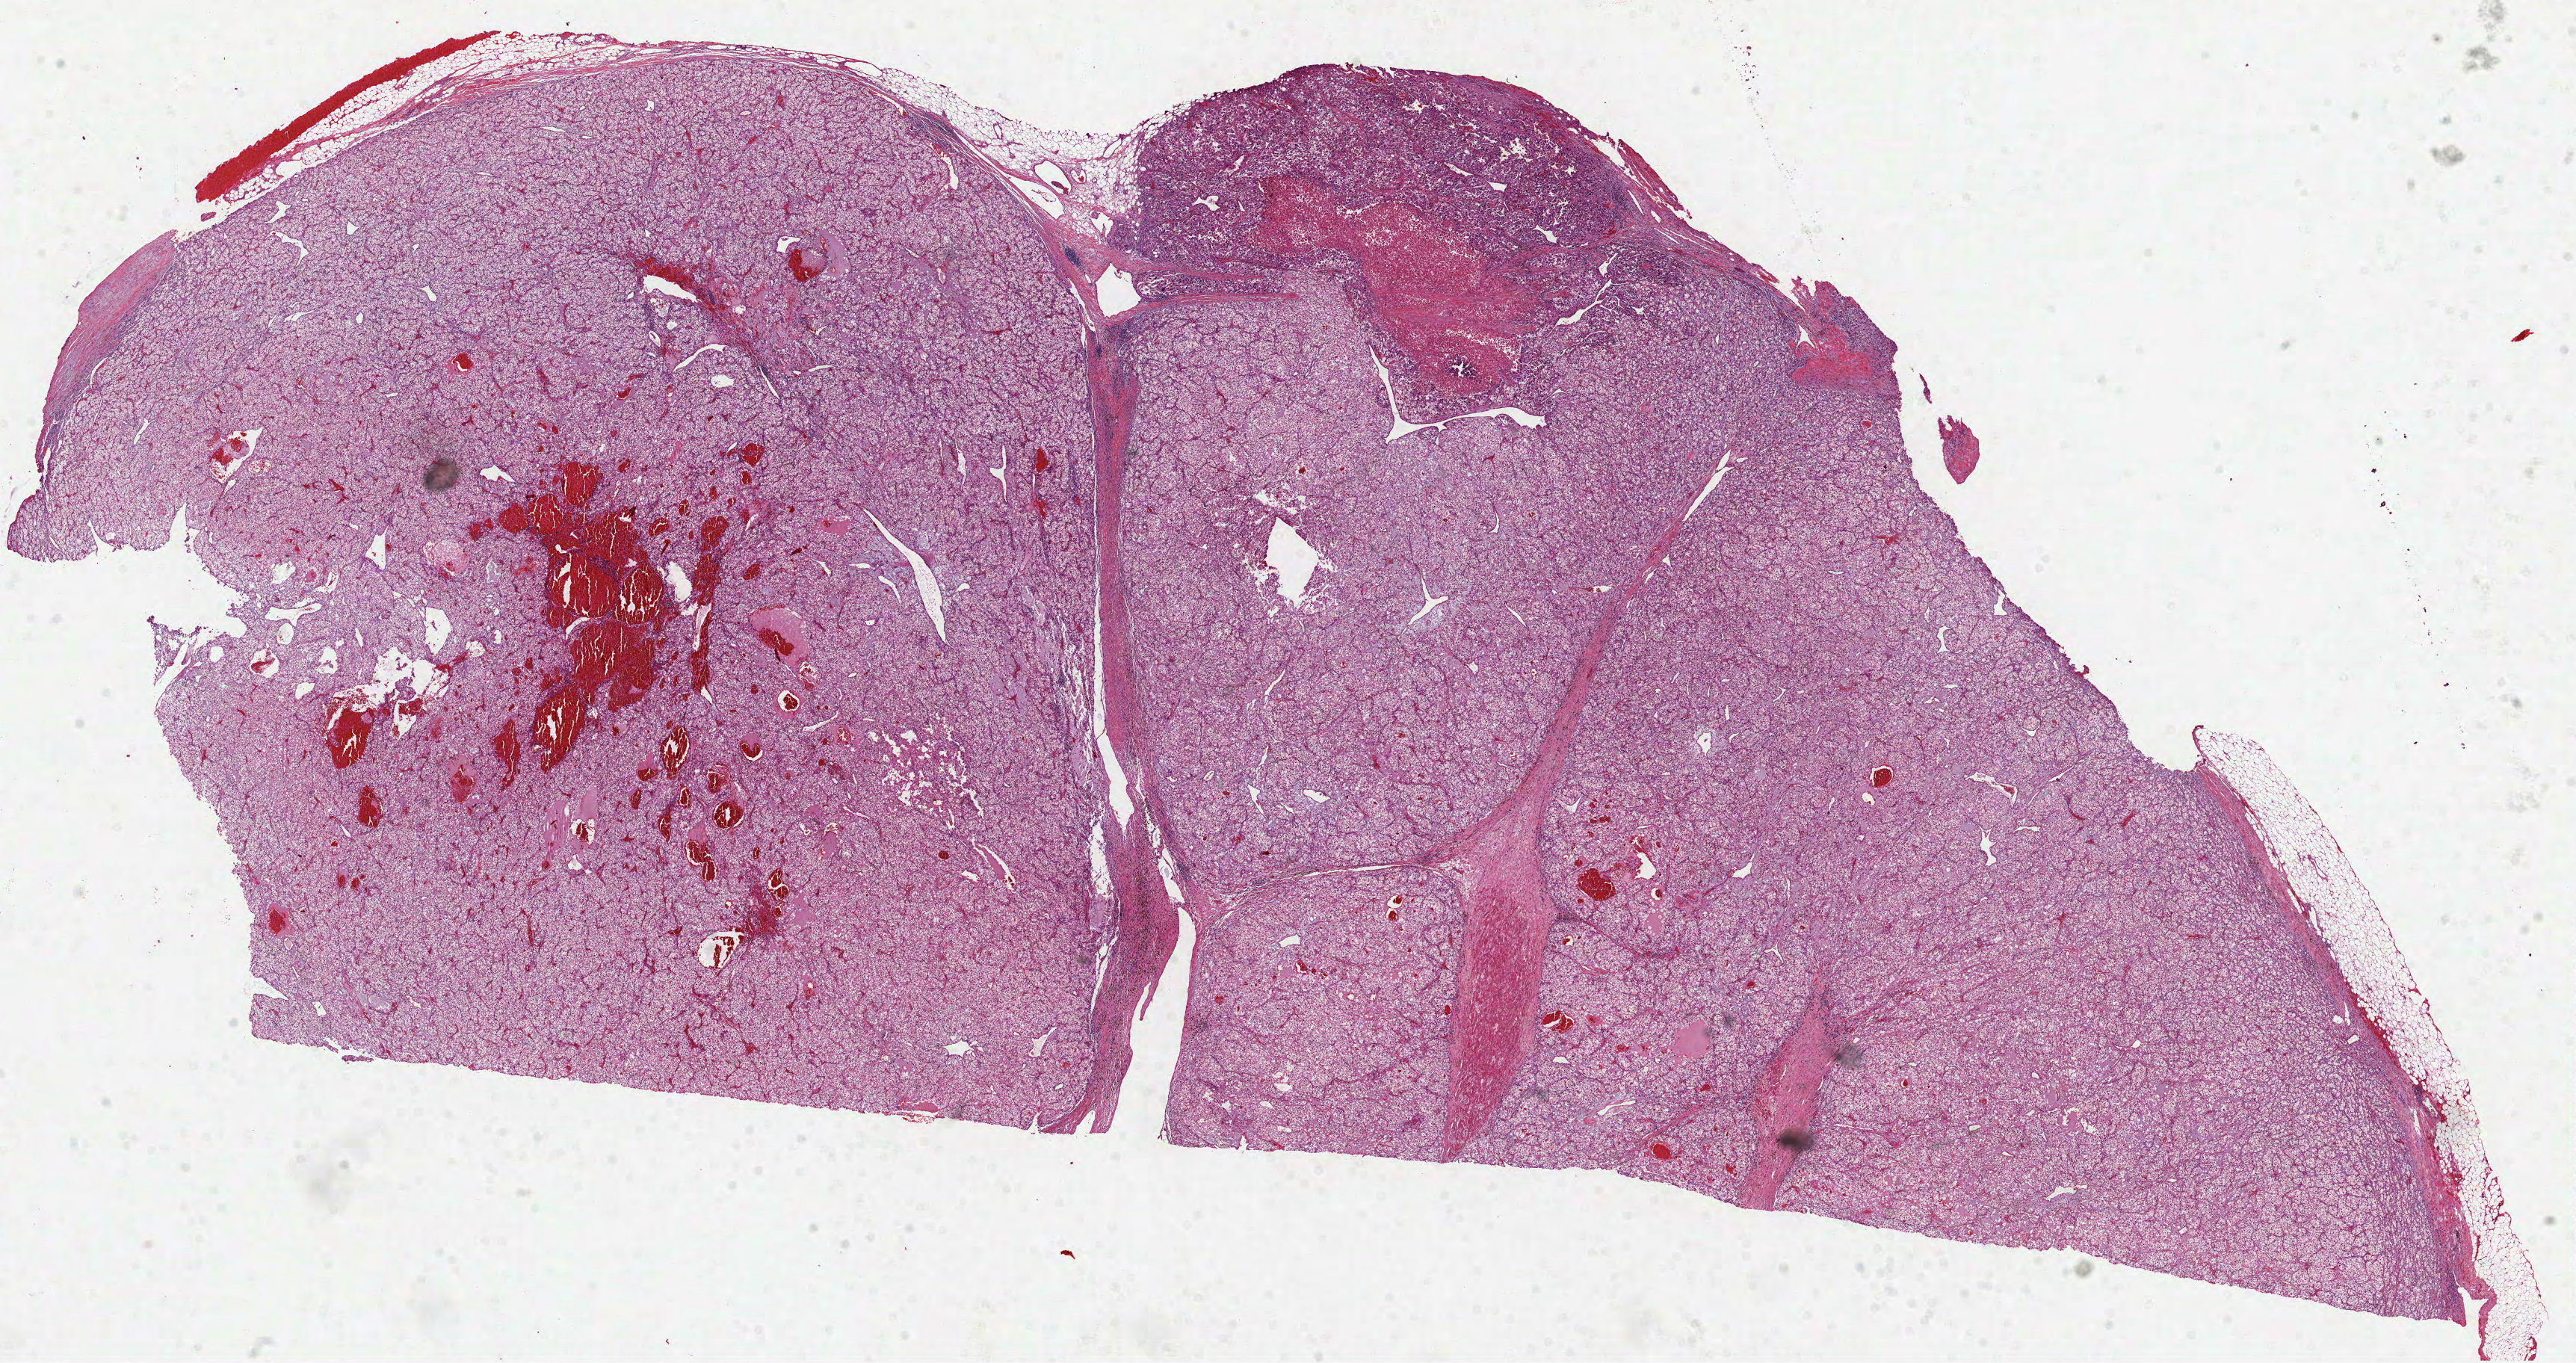
Hematoxylin and eosin (H&E) stained whole-slide image, whole scanned area (about 27.8 x 14.7 mm, from a 40x scan) shown as a low-resolution overview. Formalin-fixed paraffin-embedded (FFPE) diagnostic section. Primary tumour sample from the kidney. Patient: female, age at initial diagnosis 77 years. Histologic grade: G4 (undifferentiated).
TNM: T3b N0 M0. Histologic diagnosis: Clear cell adenocarcinoma, NOS. AJCC pathologic stage: III. Laterality: left.